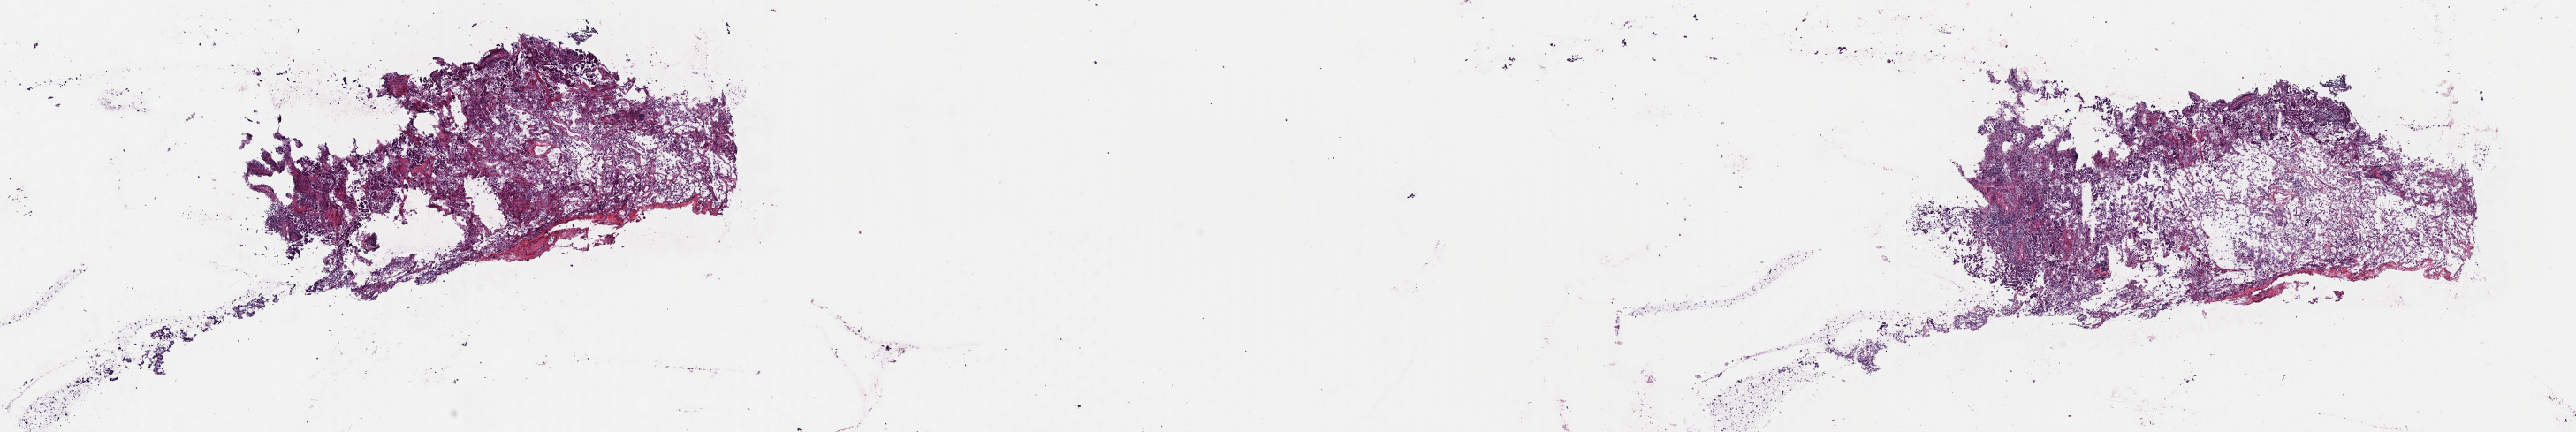
H&E whole-slide image, a low-resolution overview of the entire scanned area, about 23.0 x 3.9 mm (from a 40x scan); frozen section; primary tumour sample from the lung. Female patient; age at initial diagnosis 66 years. Slide review estimates, as recorded: tumour cells 100%, tumour nuclei 65%, normal cells 0%, stromal cells 0%, necrosis 0%. Inflammatory infiltration, as recorded: lymphocyte infiltration 3%, monocyte infiltration 3%, neutrophil infiltration 5%.
Laterality: left. AJCC pathologic stage: IA (7th edition). Histologic diagnosis: Adenocarcinoma, NOS (upper lobe, lung).